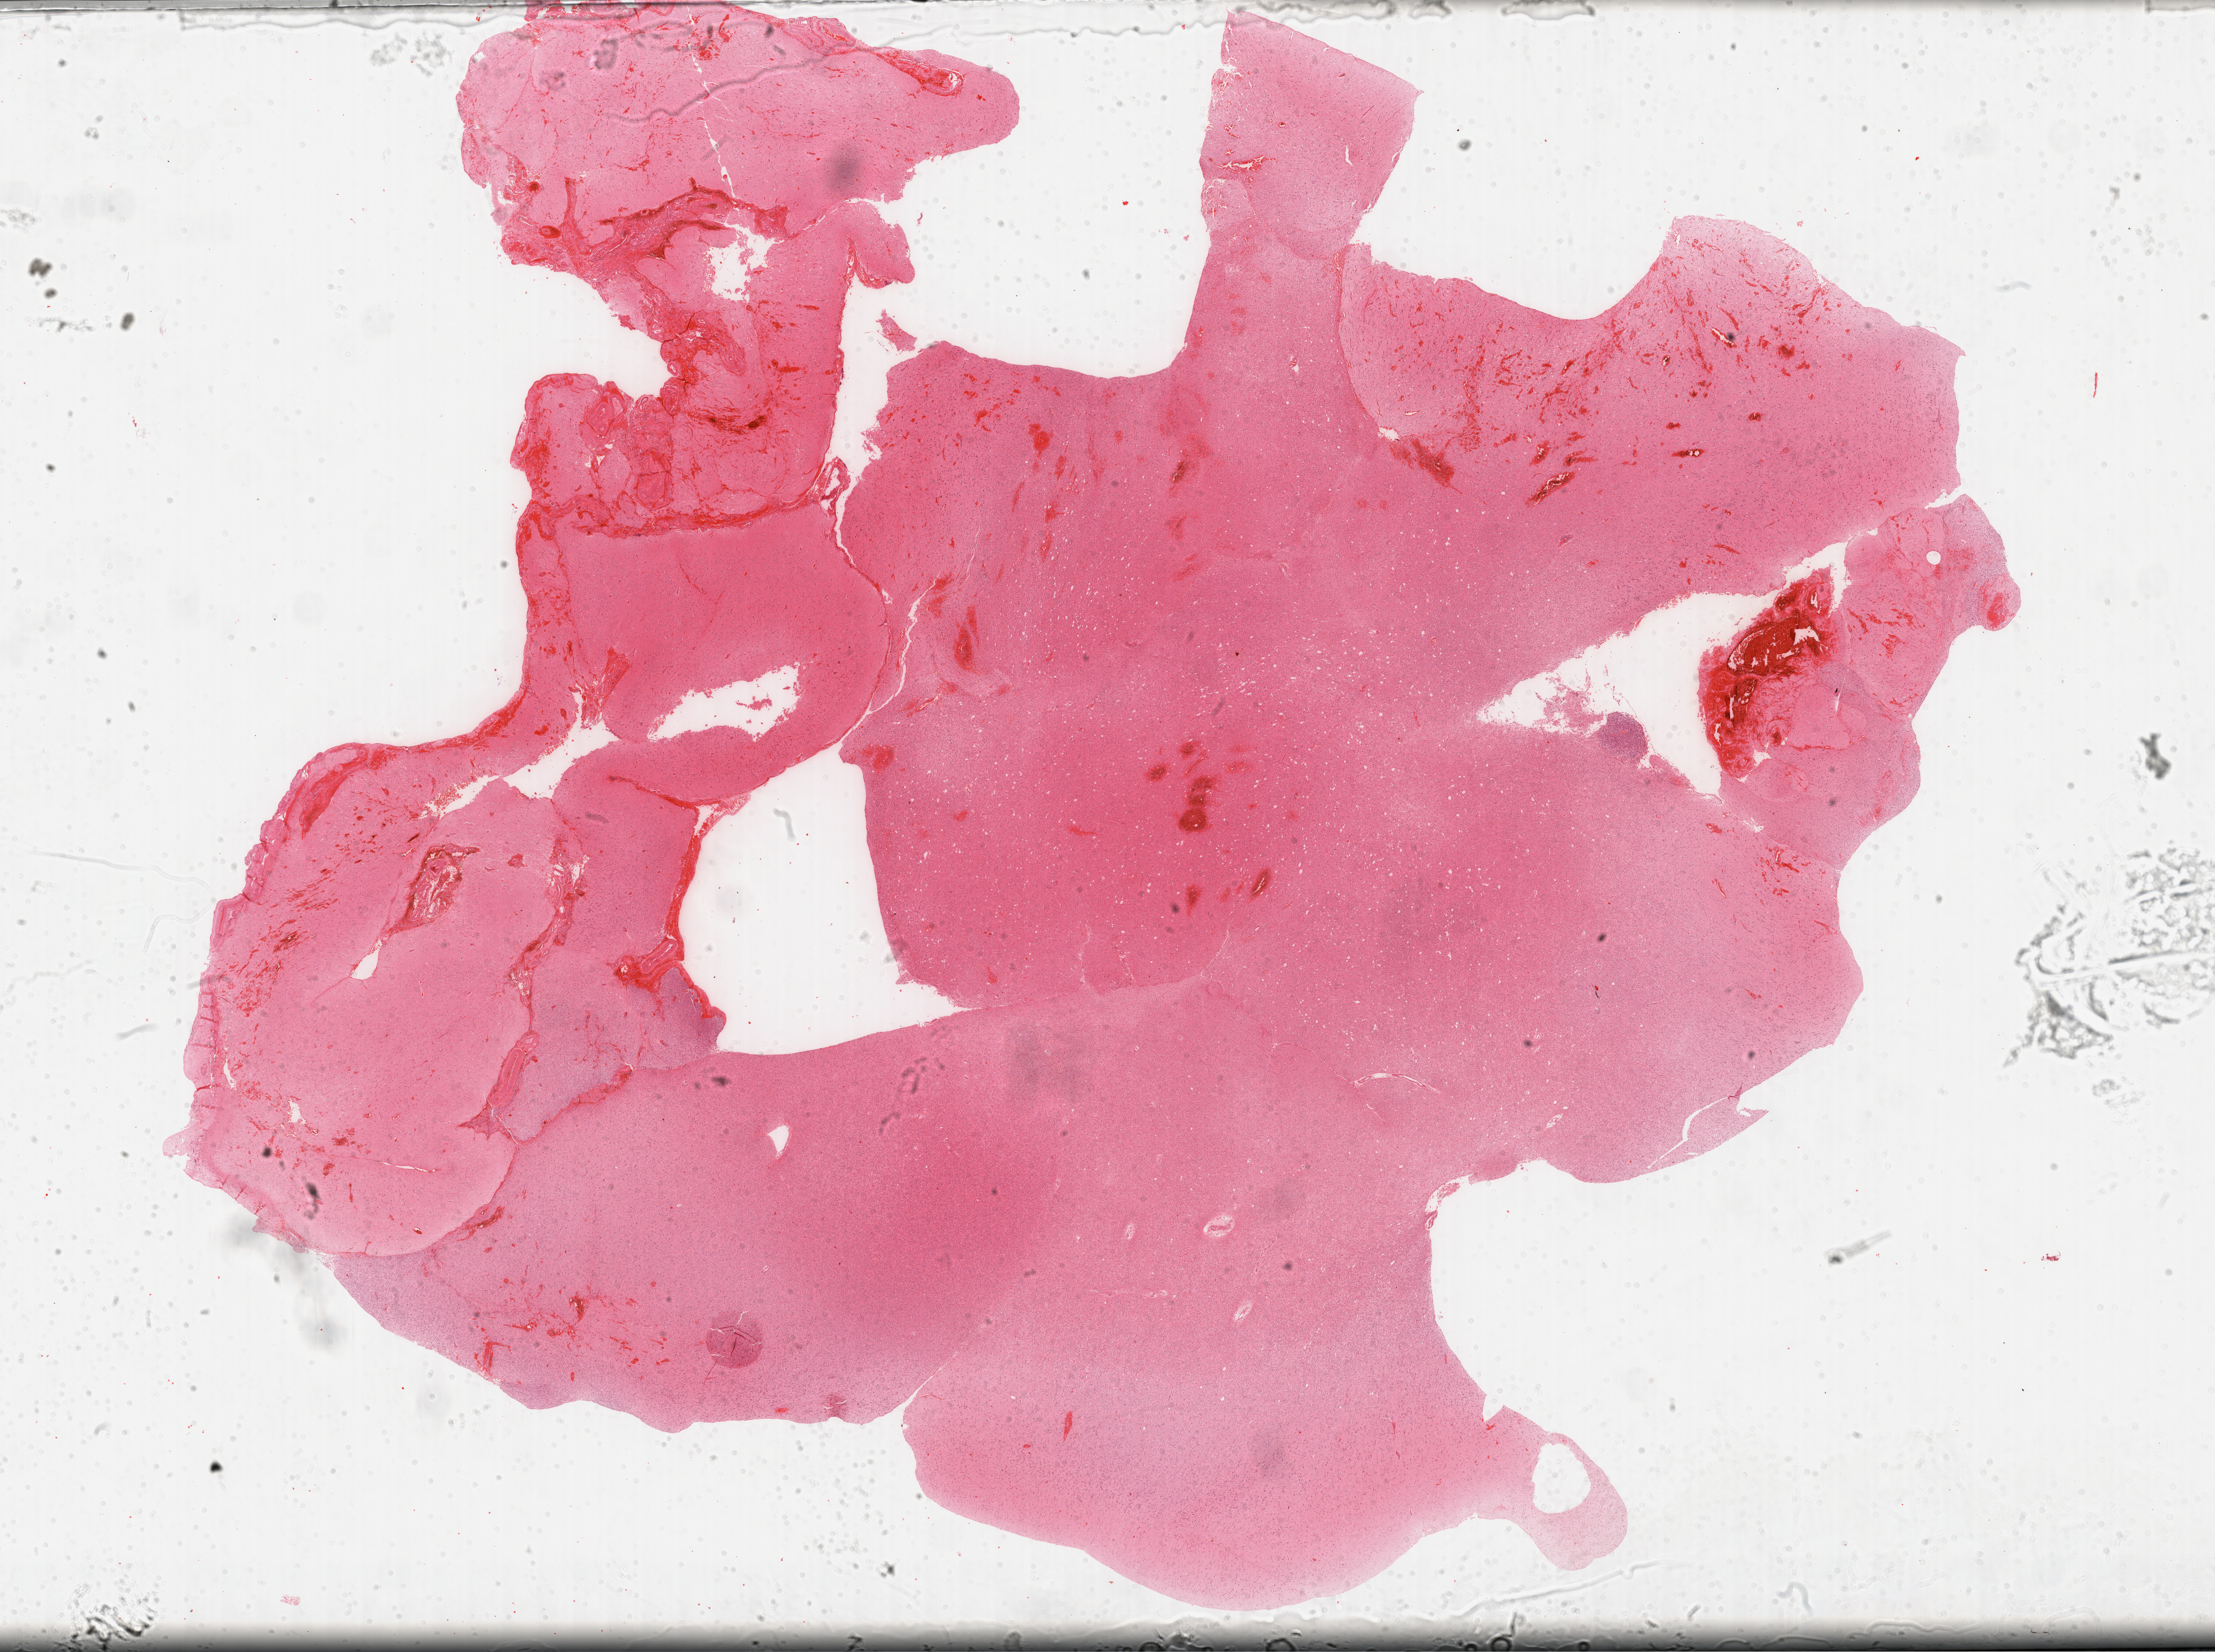
Digitized Hematoxylin and eosin (H&E) stained tissue section (whole slide), shown as a low-resolution overview of the whole scanned area (about 31.7 x 23.7 mm). Formalin-fixed paraffin-embedded (FFPE) diagnostic section. Brain, primary tumour sample. Male patient; age at initial diagnosis 58 years. Histologic grade: G3 (poorly differentiated).
* pathologic diagnosis: Oligodendroglioma, anaplastic (cerebrum)